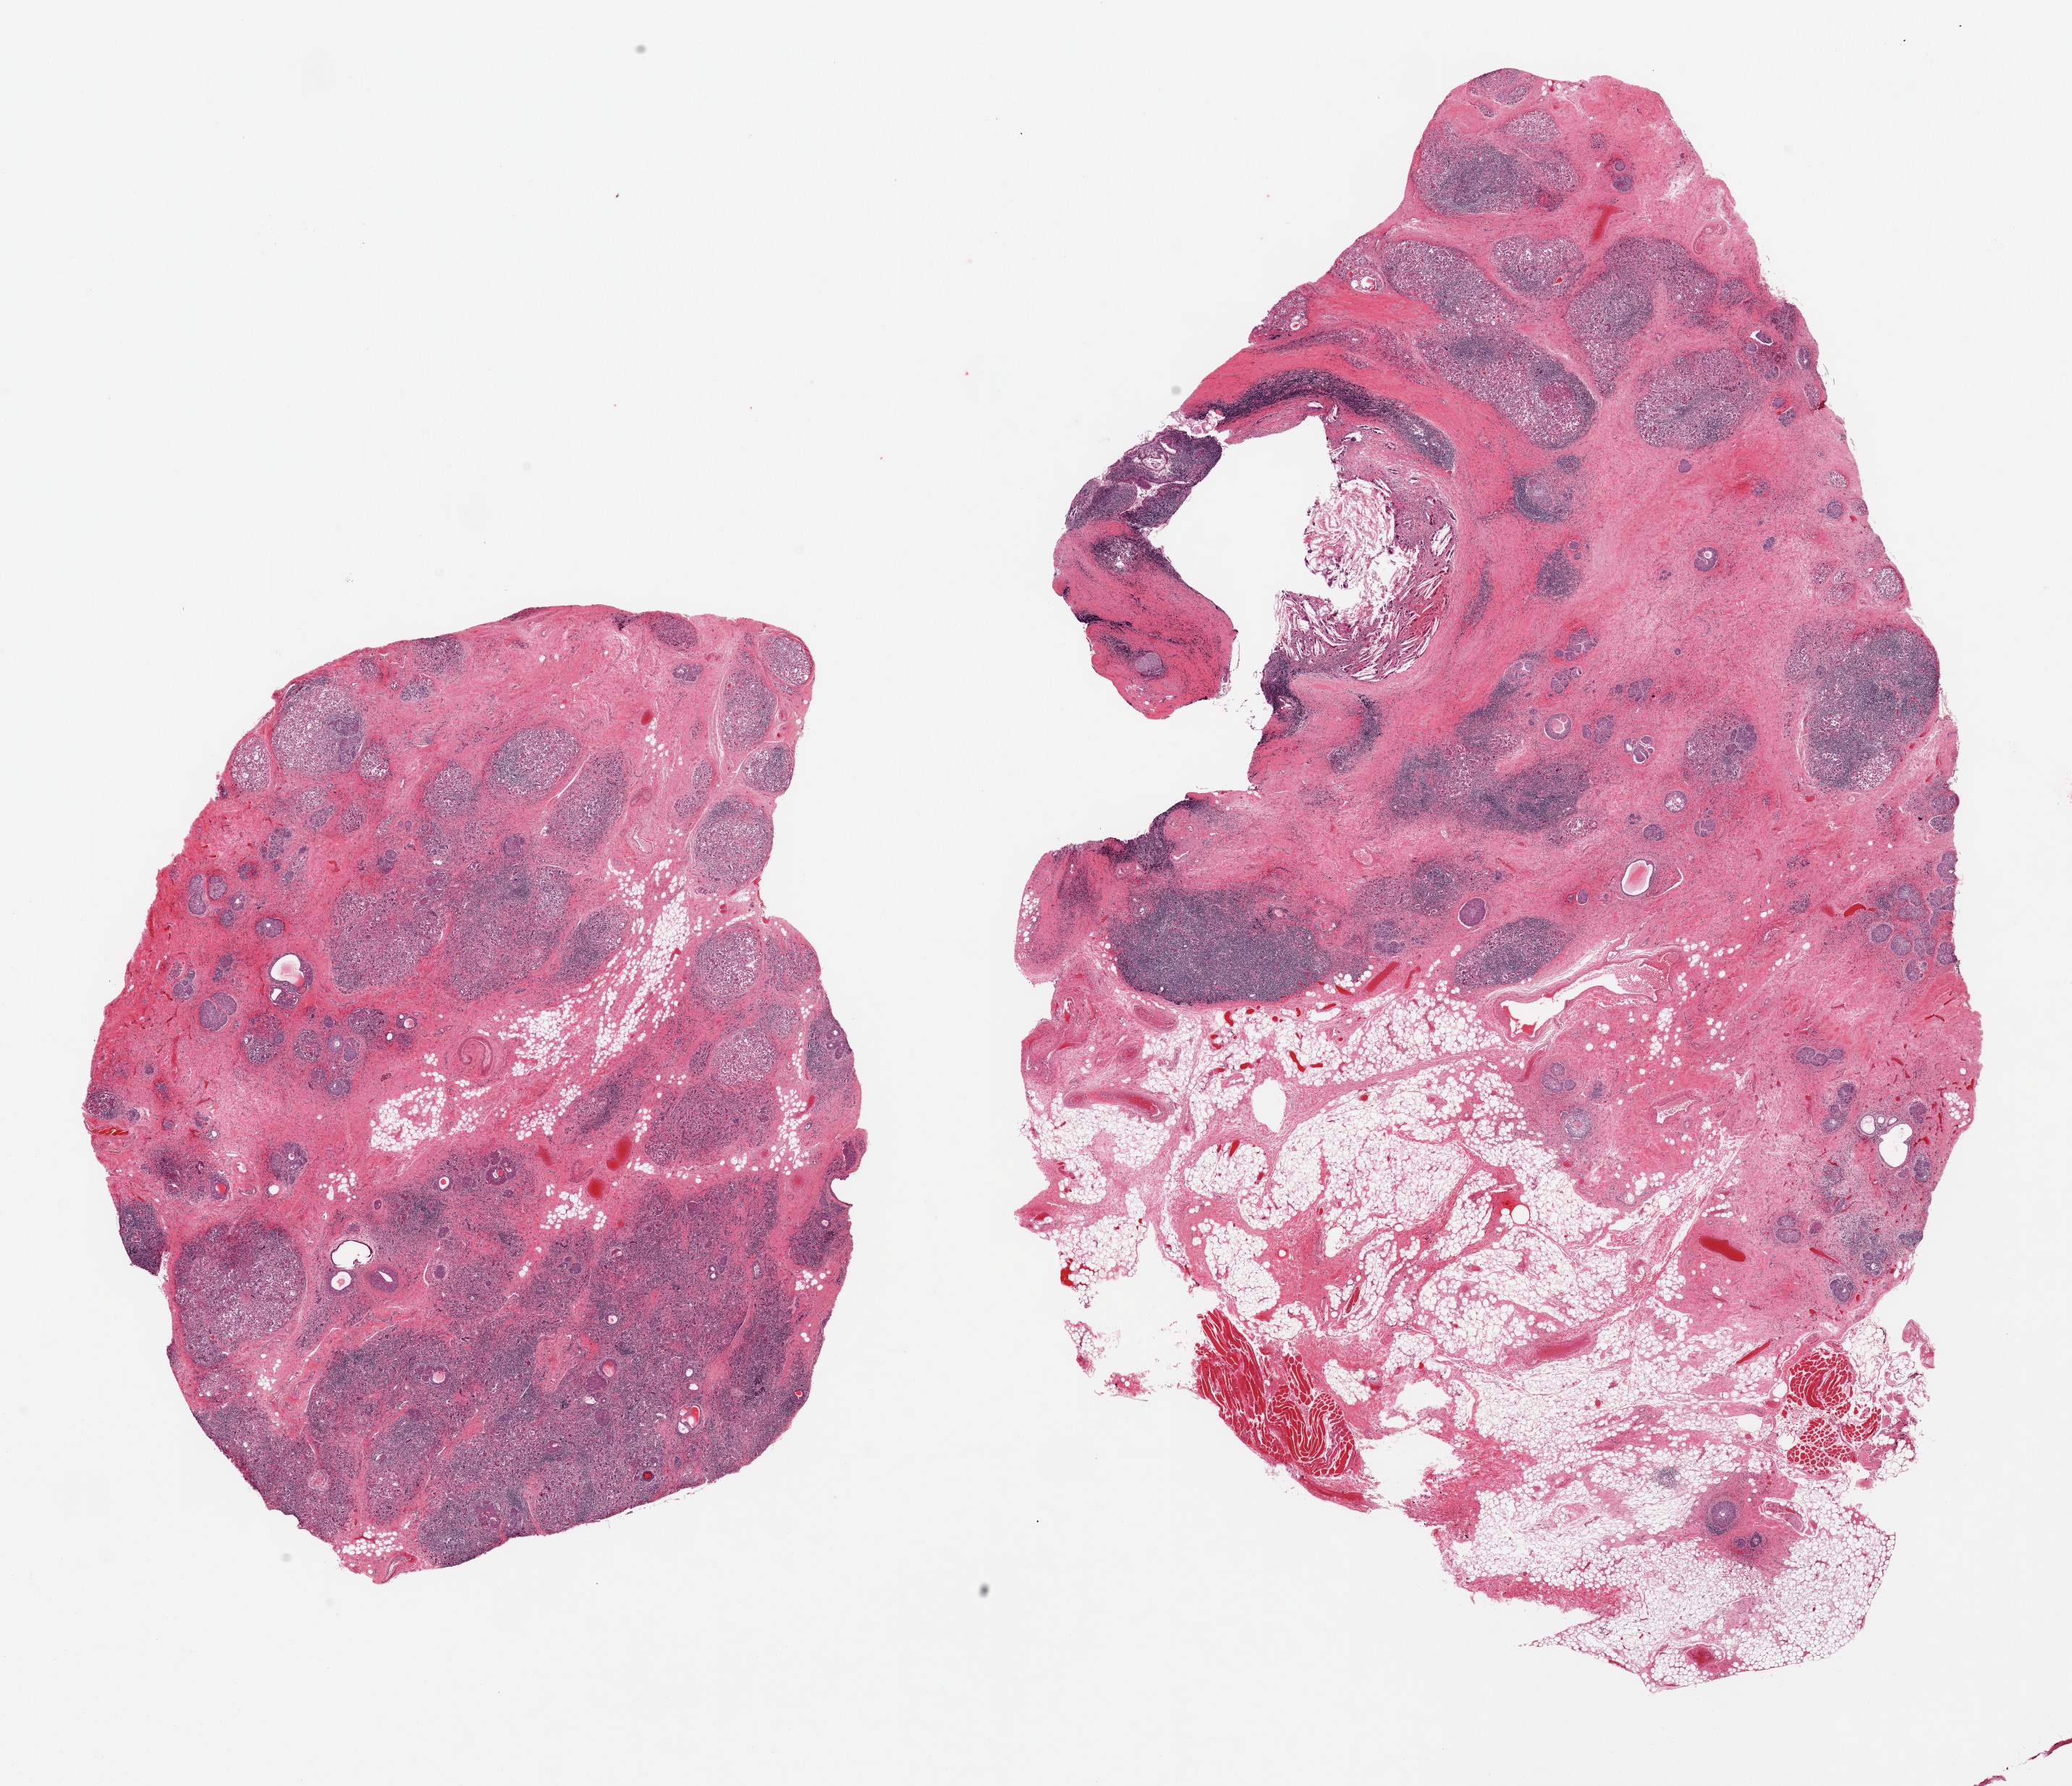
Whole-slide image, H&E stain, shown as a low-resolution overview of the whole scanned area (about 22.6 x 19.5 mm, slide scanned at 20x); PAXgene-fixed, paraffin-embedded tissue; section of thyroid (target tissue); tissue donor sample.
Pathologist's review note for this sample: 2 pieces, end-stage Hashimoto's thyroiditis with prominent regressive change, ~20% adherent fat.